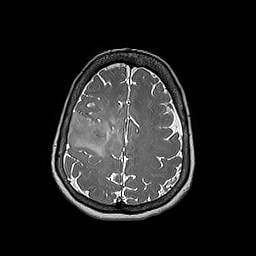
Brain MRI from a brain-tumour surgery series, one axial slice; slice 65 of 192 in the series (ordered by position); 1 mm slice thickness; 256 × 256 image matrix. From the clinical record (not read from this slice): histopathology: Oligodendroglioma; WHO grade: 3; IDH mutation: yes.
Structures marked on this image (expert manual segmentation):
- tumour: bounding box (x1, y1, x2, y2) in pixels: (67, 112, 108, 148)